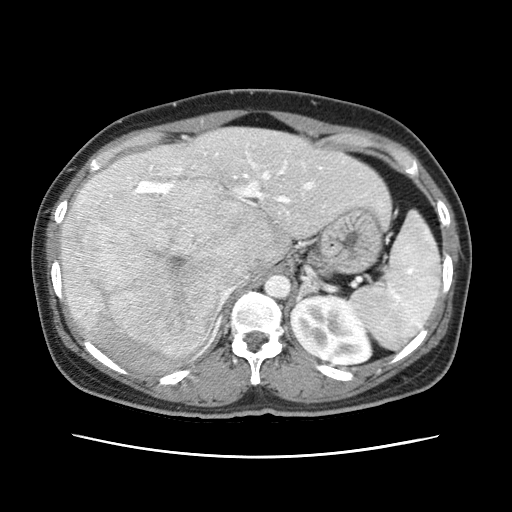
Contrast-enhanced abdominal CT (liver protocol), one axial slice; slice 41 of 79 in the series (ordered by position); reconstruction kernel STANDARD; soft-tissue window (W 400 / L 40 HU); 512 × 512 image matrix. Case-level facts recorded for this patient, not image findings: diagnosis: hepatocellular carcinoma (patient treated with transarterial chemoembolisation; whether this scan precedes or follows treatment is not stated here); TNM stage (as recorded): Stage-I; Child-Pugh class: A; tumour nodularity: uninodular.
Structures marked on this image (semi-automatic segmentation, software-assisted and operator-edited):
- abdominal aorta: bounding box (x1, y1, x2, y2) in pixels: (265, 273, 291, 299)
- liver parenchyma outside the tumour (the mass and vessels are separate outlines, so this box may not span the whole liver): (60, 128, 388, 358)
- mass: (69, 182, 278, 360)
- liver vessels: (80, 153, 321, 325)